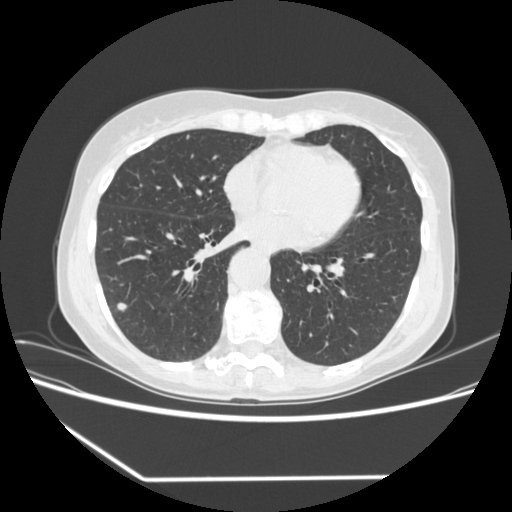
Low-dose screening chest CT, one axial slice; slice 156 of 323 in the series (ordered by position); reconstruction kernel STANDARD; lung window (W 1500 / L -600 HU); 1.25 mm slice thickness; 512 × 512 image matrix, field of view 360 × 360 mm.
Outlined on this slice (manually delineated by an expert):
- lesion 2 (nodule, lower lobe of right lung): bounding box [x1, y1, x2, y2] px = [117, 303, 127, 312]